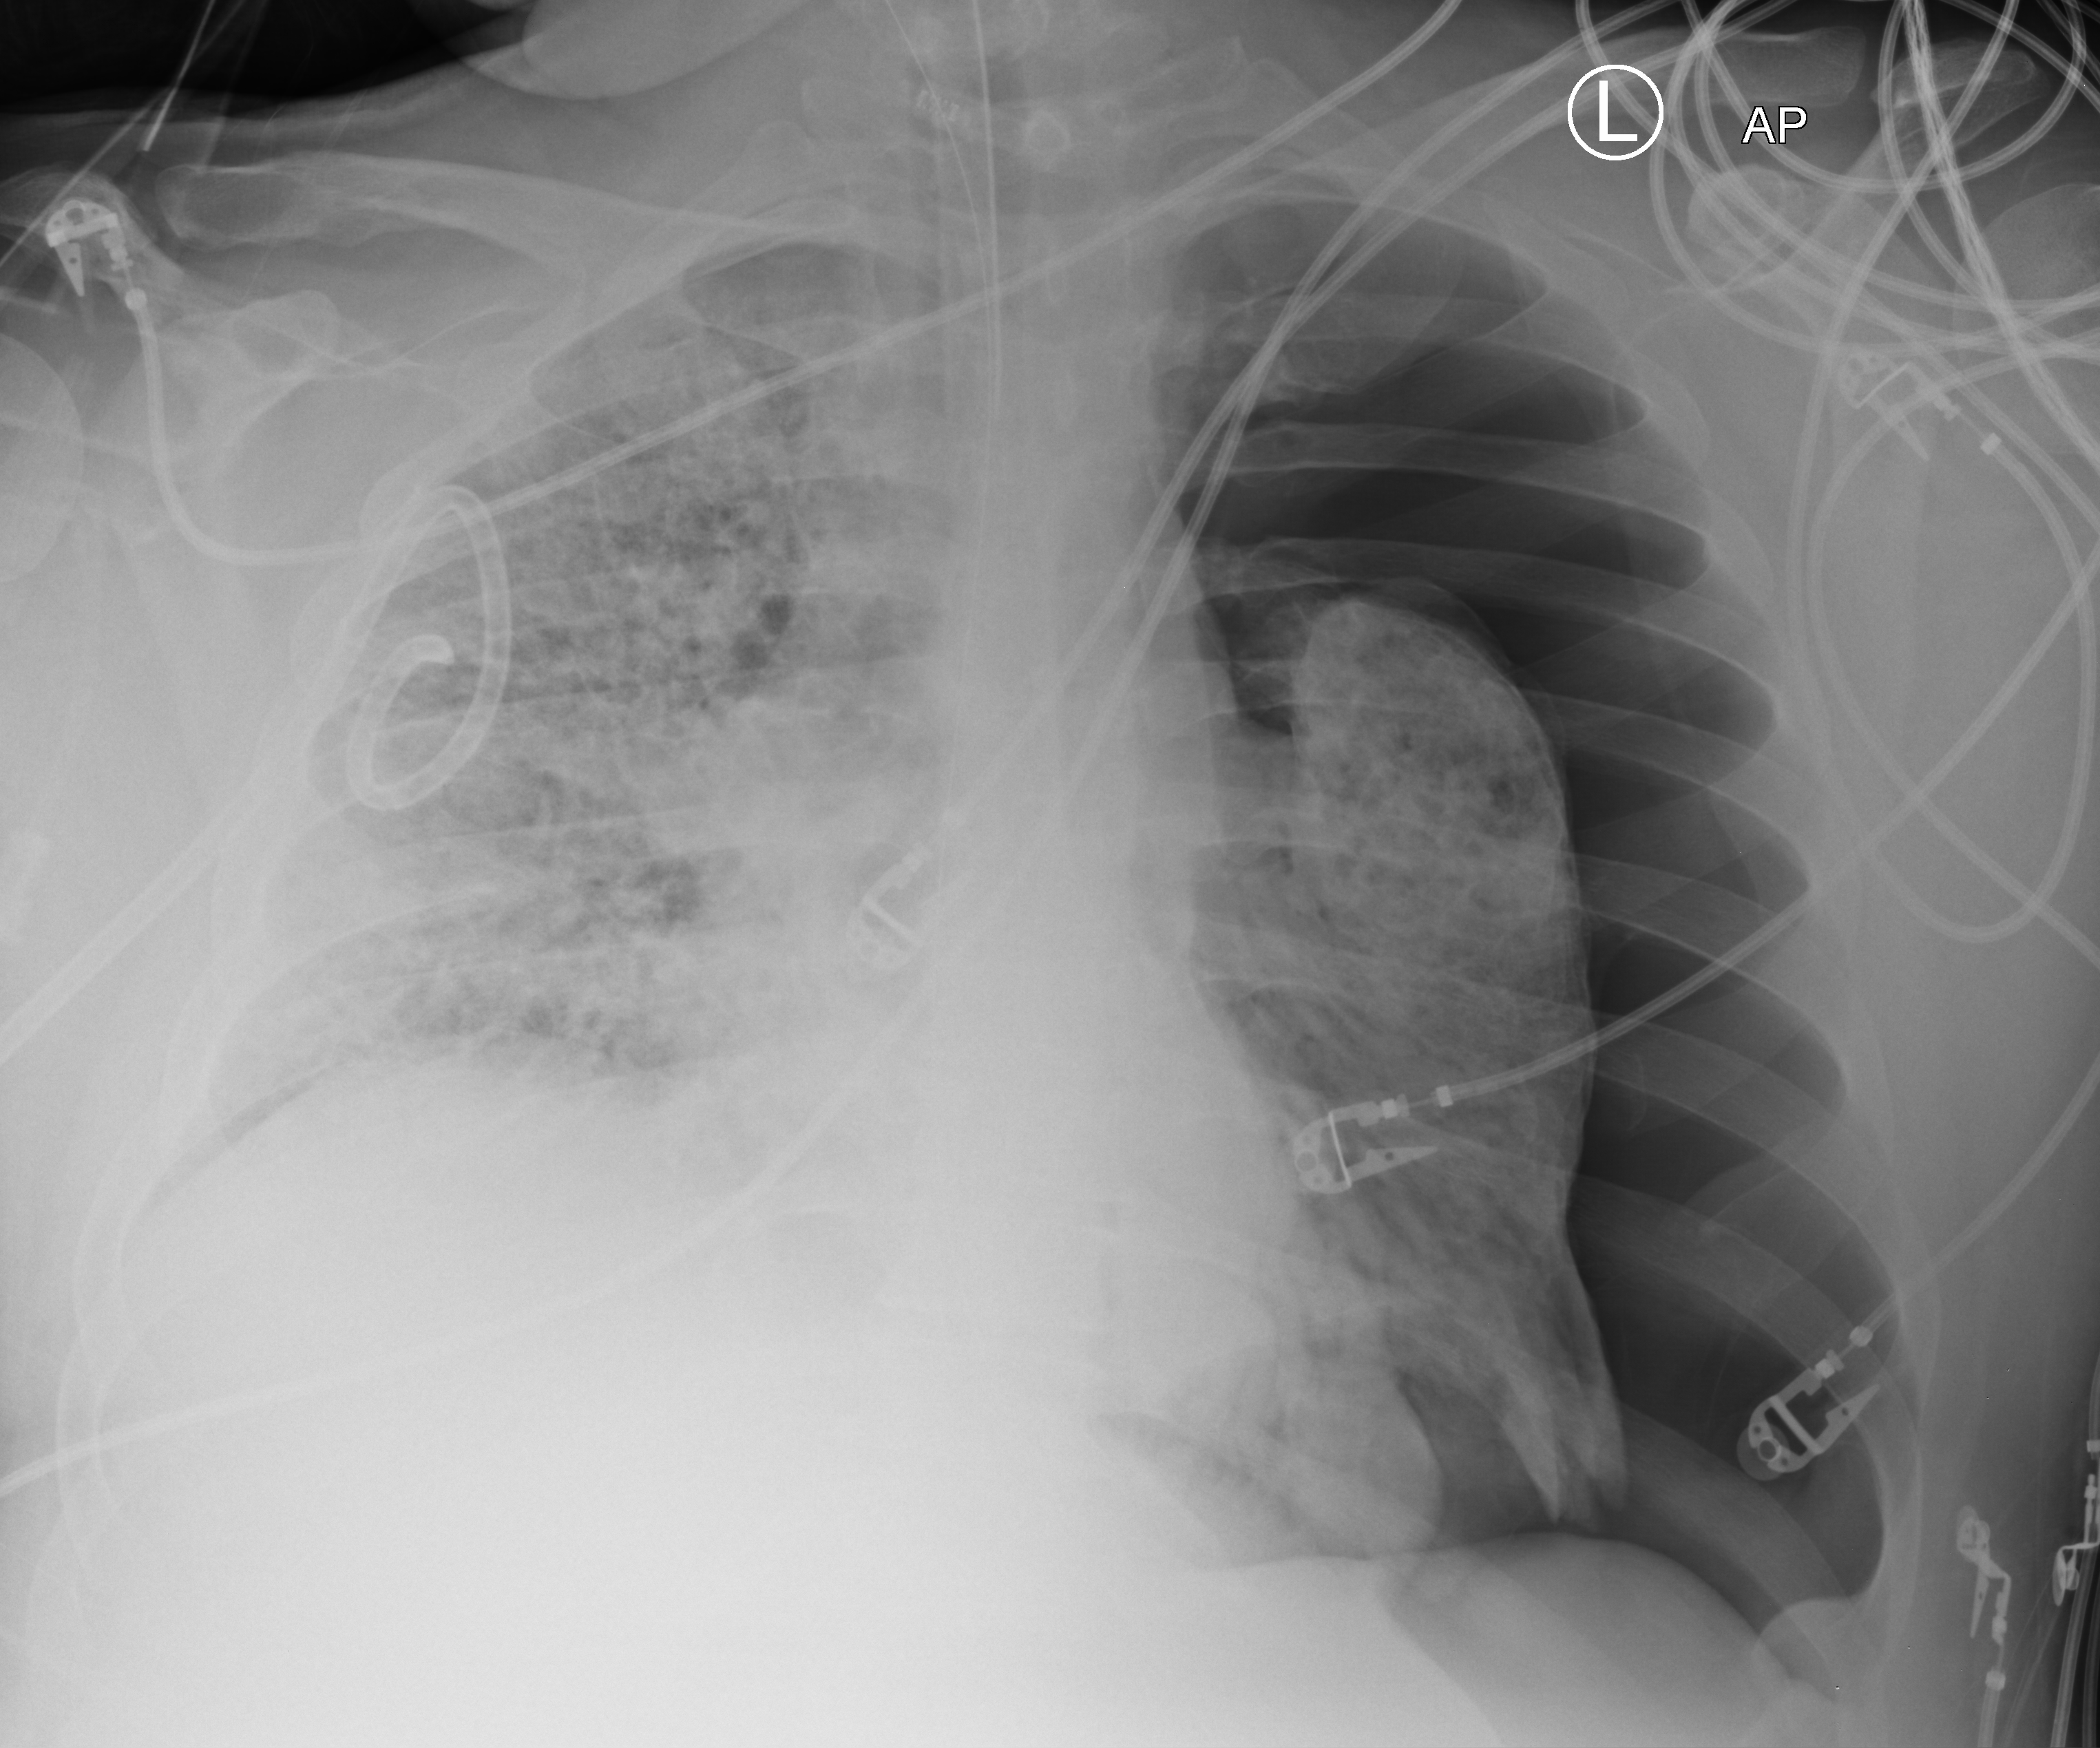
Portable chest radiograph, anteroposterior (AP) projection. Adult patient hospitalised with COVID-19, age 18–59 years.
Hospital-stay facts (about this admission, not read from this image; timing relative to this image not recorded): admitted to intensive care during this hospital stay: yes.